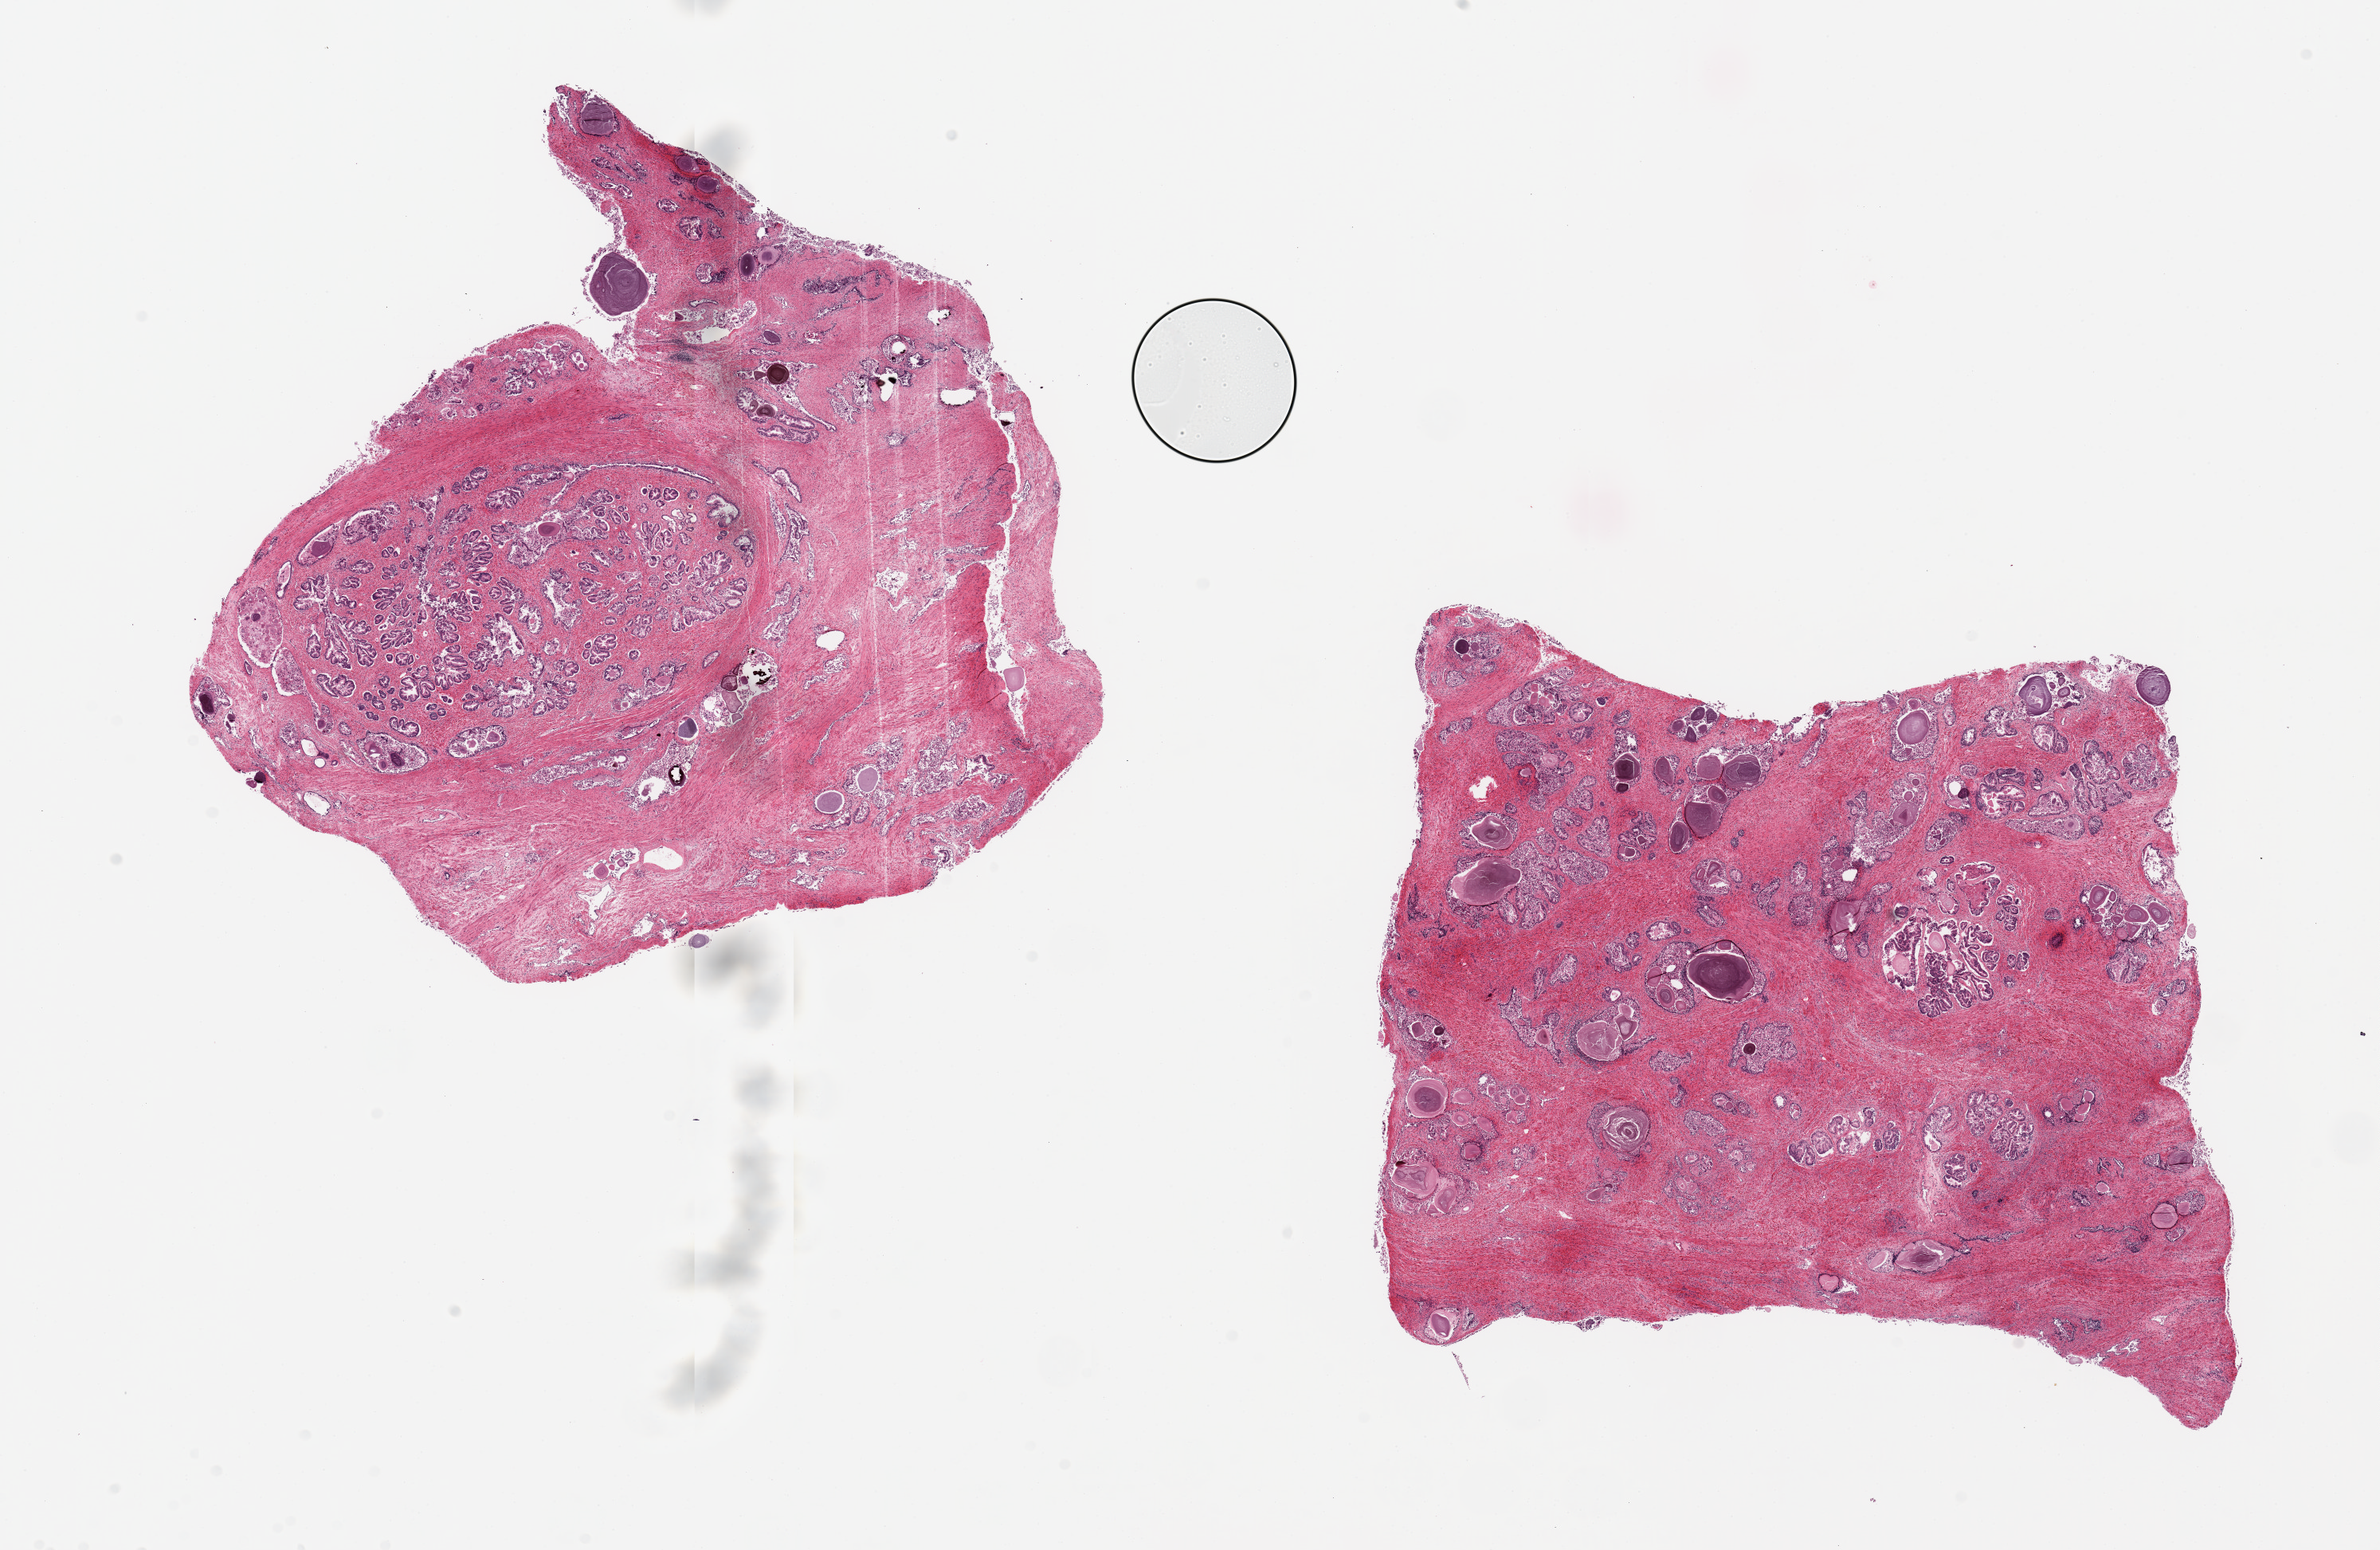
Whole-slide image, H&E stain, brightfield, whole scanned area (about 23.6 x 15.4 mm) shown as a low-resolution overview. PAXgene-fixed paraffin-embedded (PFPE) section. Target tissue: prostate. Tissue donor sample. Donor sex: male.
Pathologist's review note for this sample: 2 pieces, 9x9 & 8.5x8mm; glands 2 to 3; stroma= 1 (autolysis).